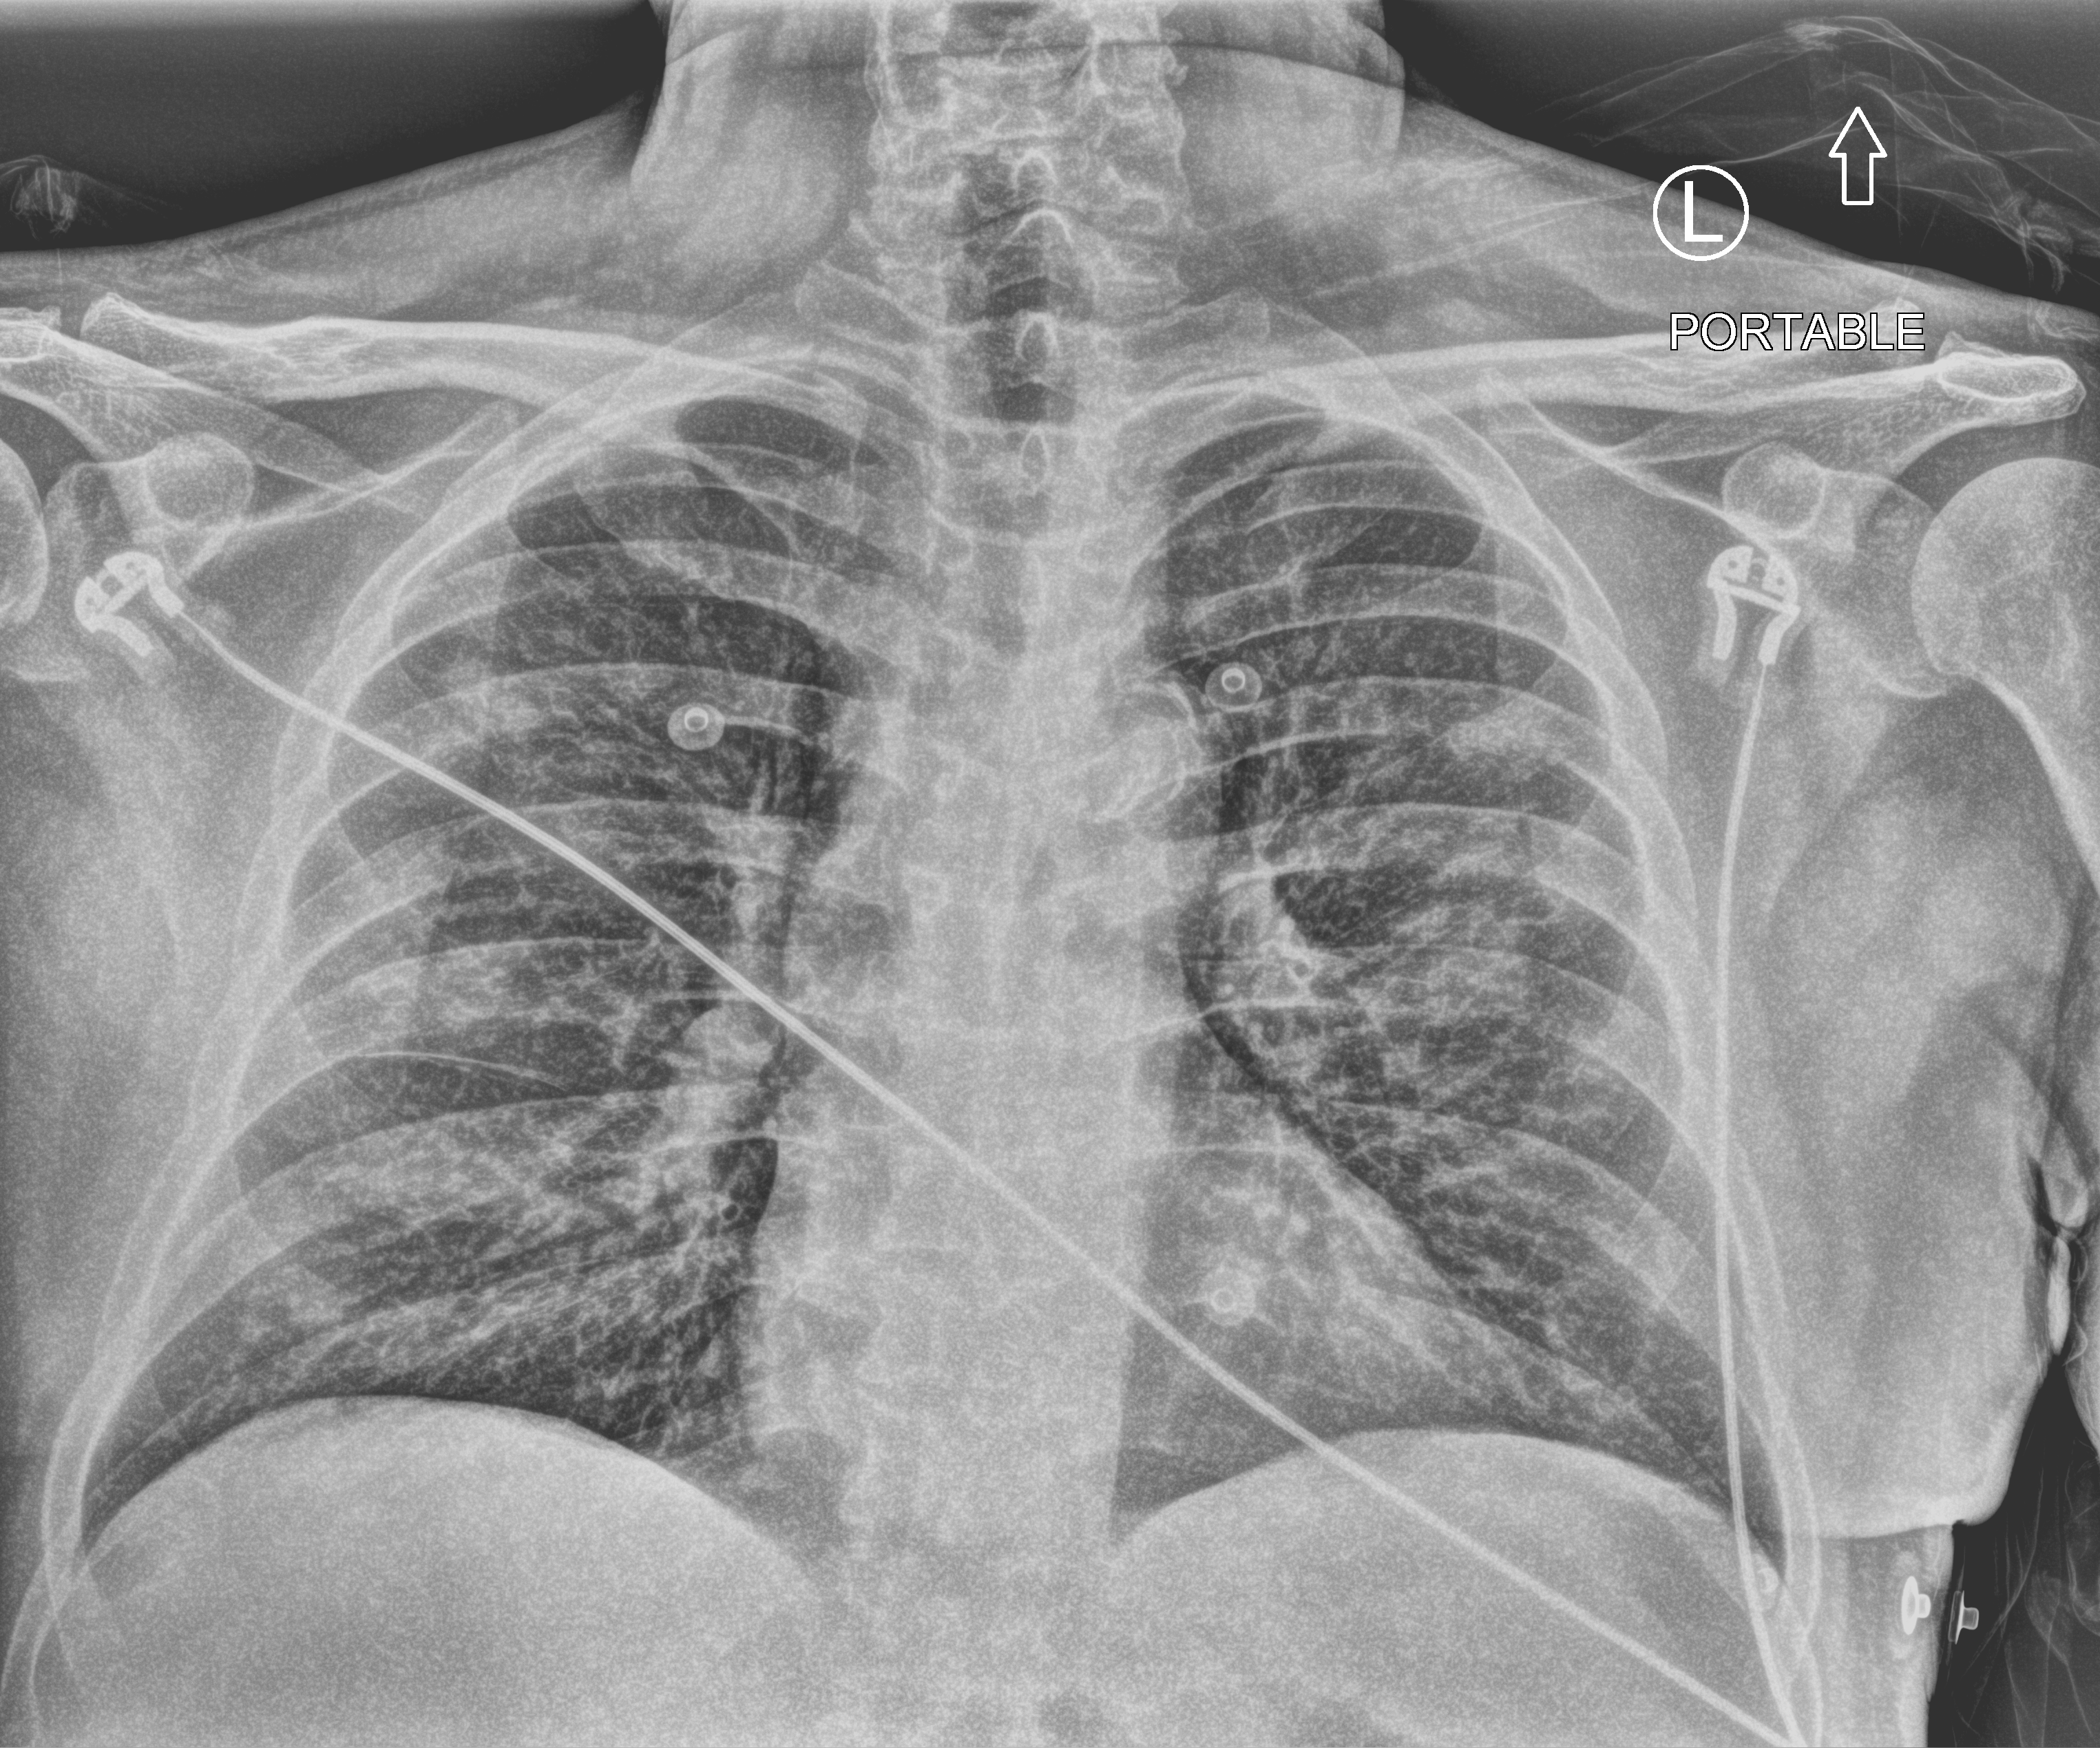
Chest X-ray (portable); anteroposterior (AP) projection. Male patient hospitalised with COVID-19, age 60–74 years.
Admission-level facts for this patient (not findings on this image; timing relative to this image not recorded): mechanically ventilated during this hospital stay: no; admitted to intensive care during this hospital stay: no.